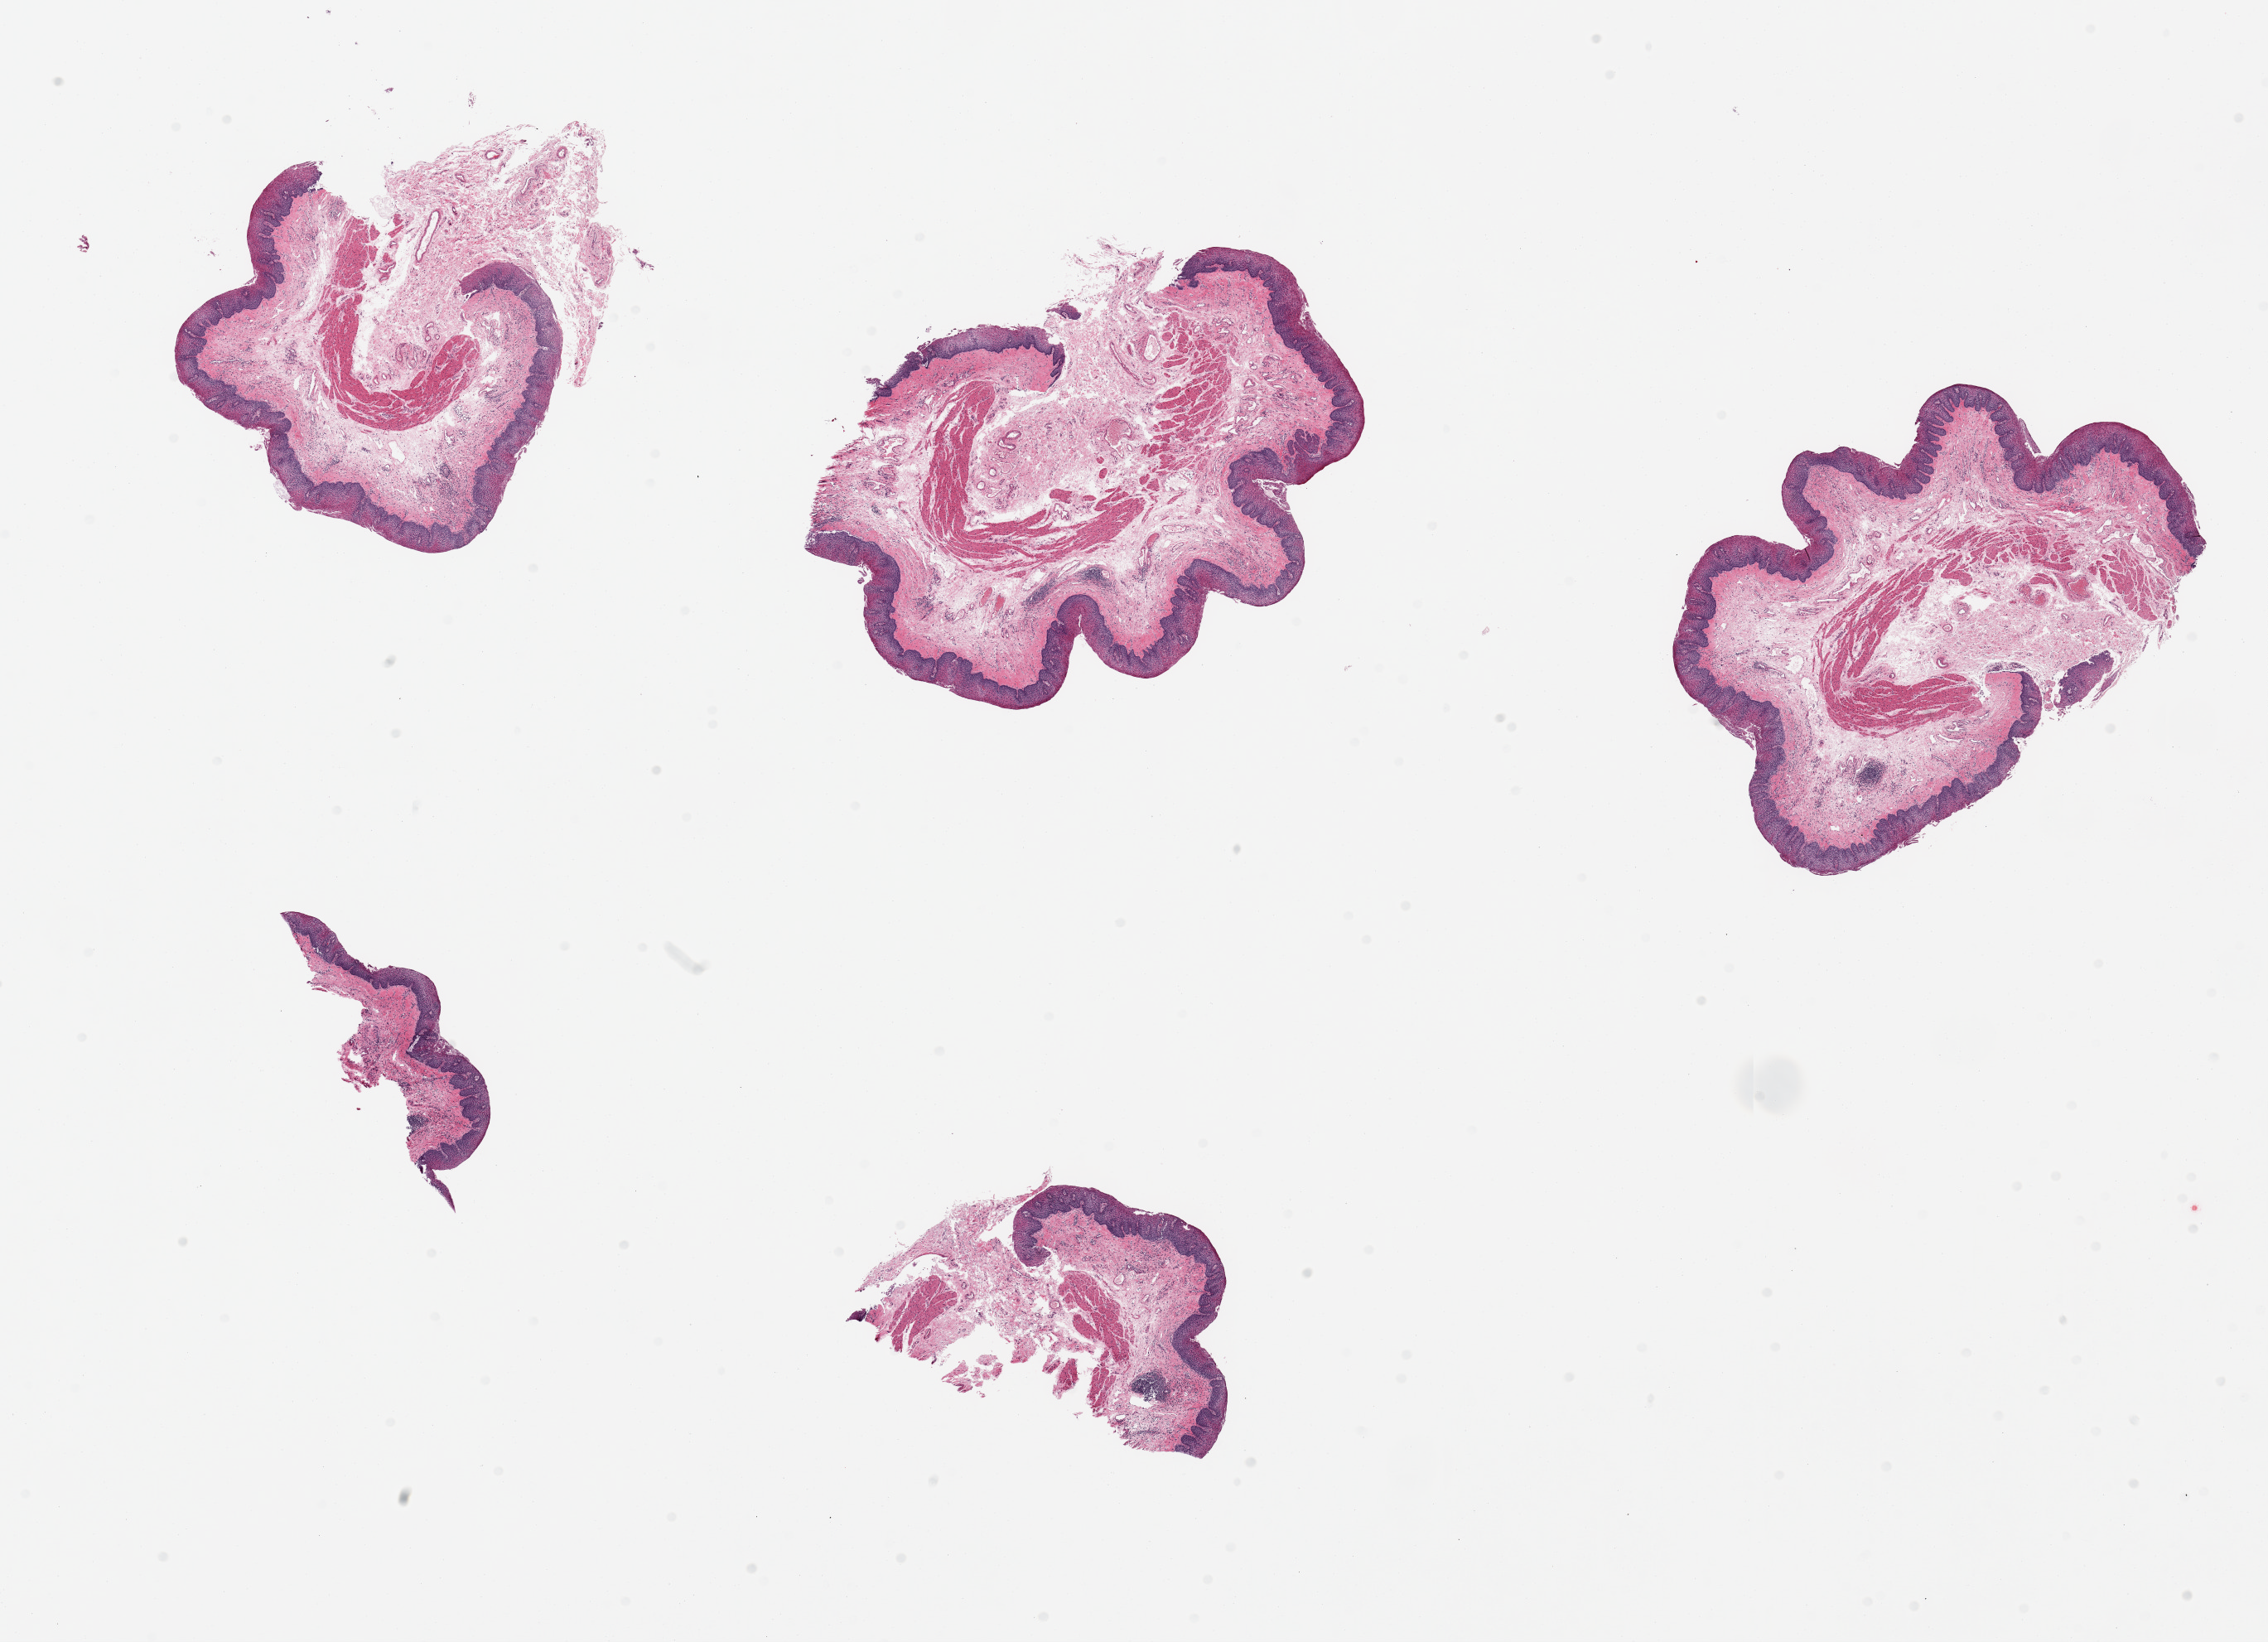
Whole-slide image, haematoxylin and eosin stain, low-resolution overview of the scanned area, about 21.7 x 15.7 mm, PAXgene-fixed, paraffin-embedded tissue, target tissue: esophageal mucous membrane, donor tissue sample.
• pathologist's review note for this sample: 6 pieces; focal surface sloughing